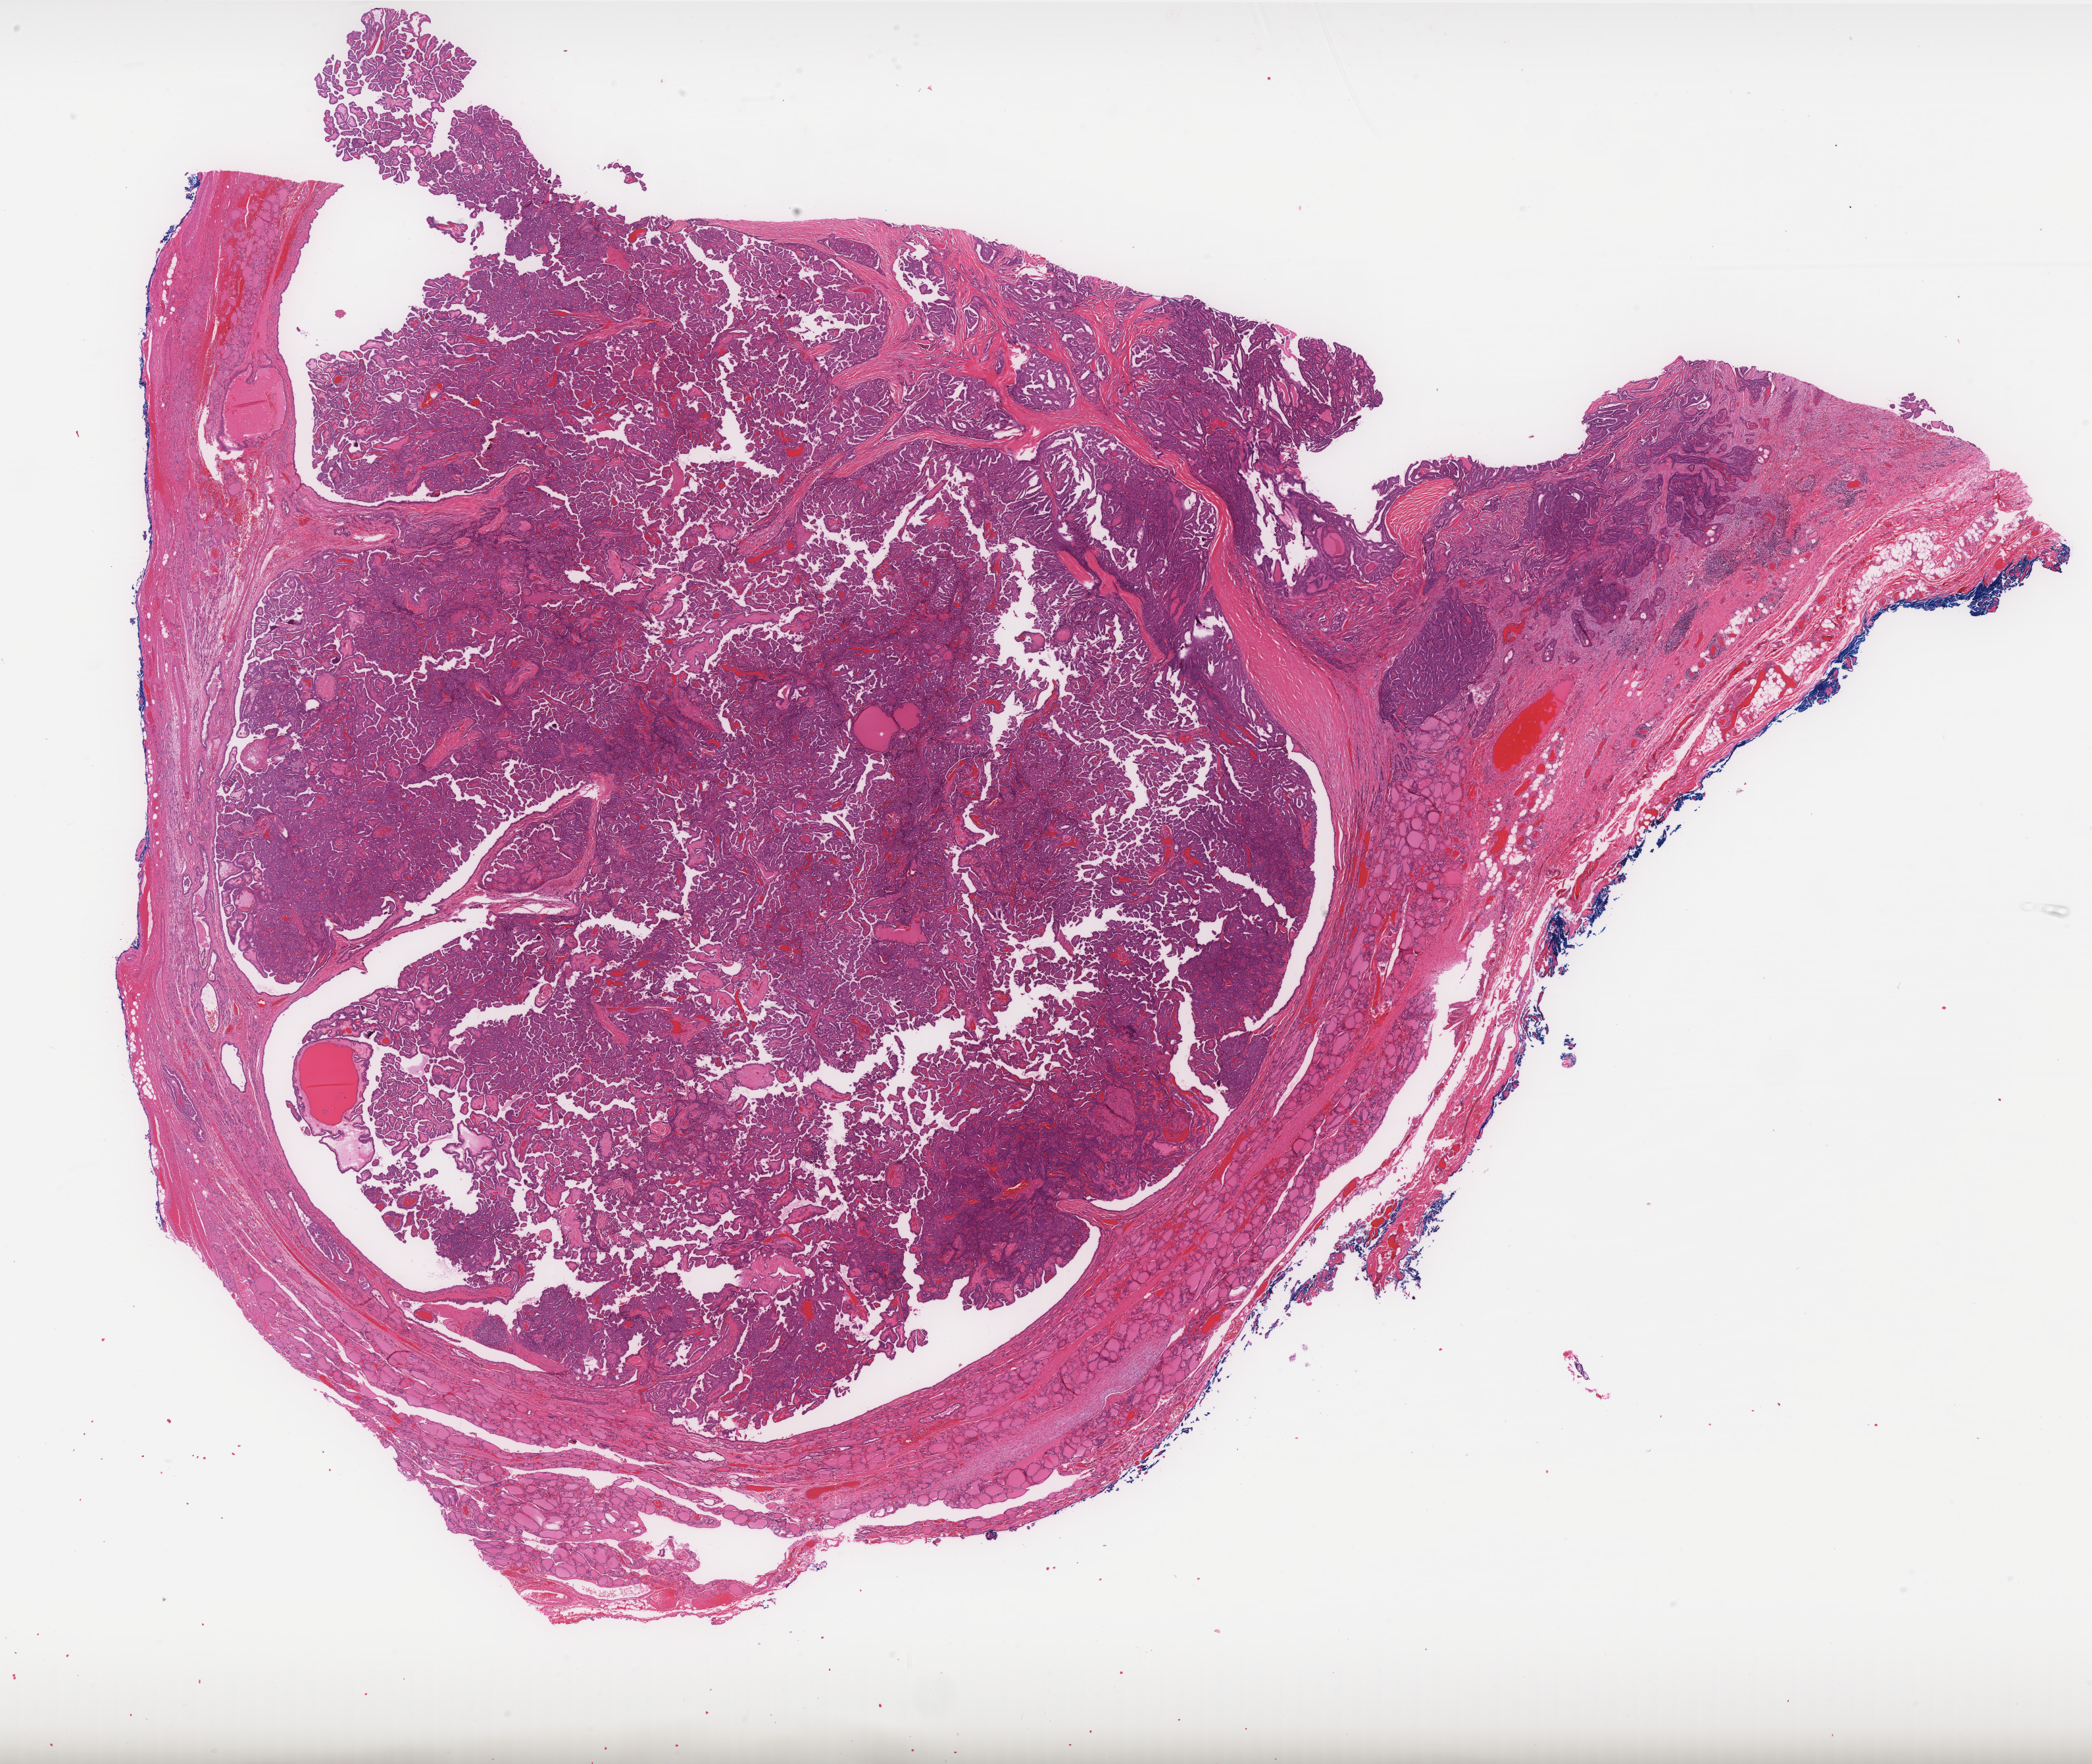
Digitized H&E-stained tissue section (whole slide), shown as a low-resolution overview of the whole scanned area (about 25.5 x 21.5 mm, from a 40x scan), FFPE section, primary tumour sample from the thyroid. Female, age 23 years at initial diagnosis.
Diagnosis: Papillary carcinoma, follicular variant (thyroid gland). Laterality: left. AJCC pathologic stage: I (6th edition).